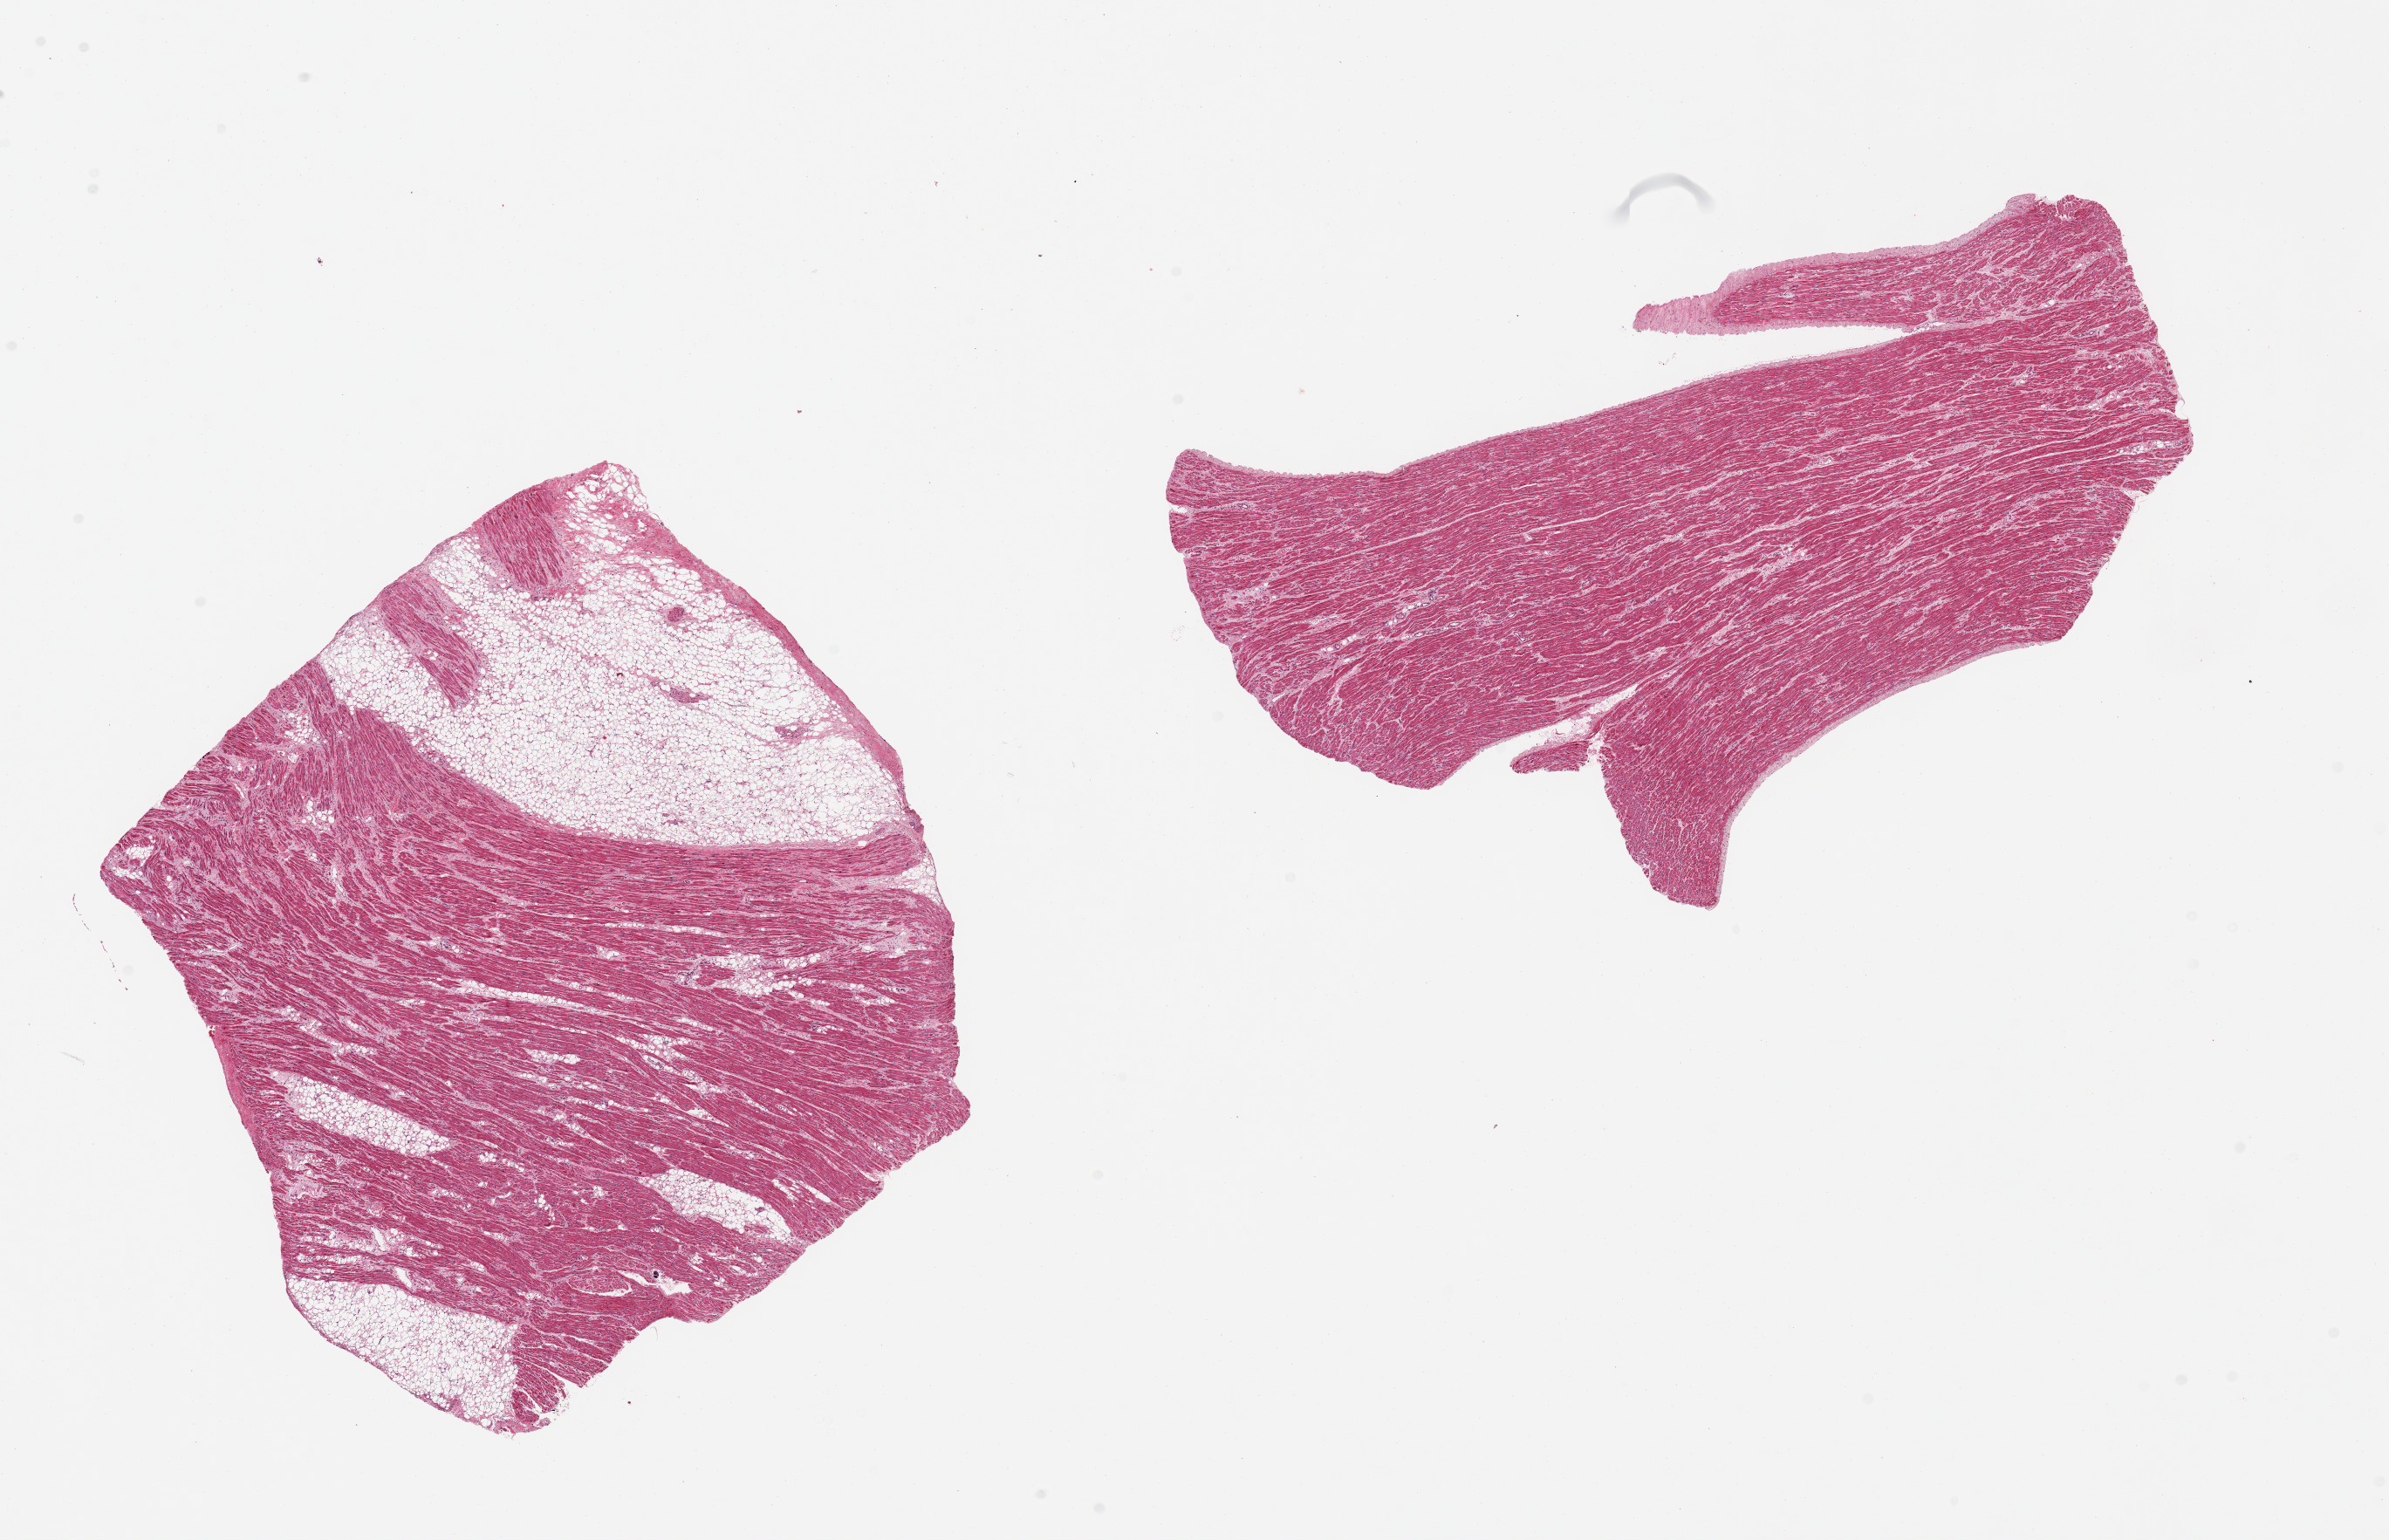
Whole-slide image, haematoxylin and eosin stain, a low-resolution overview of the entire scanned area, about 21.7 x 14.0 mm (acquisition: 20x scan); PAXgene-fixed paraffin-embedded (PFPE) section; section of auricular appendage (target tissue); donor tissue sample. Female donor.
Pathologist's review note for this sample: 2 pieces: 1 free of fat, other has 40% fat.